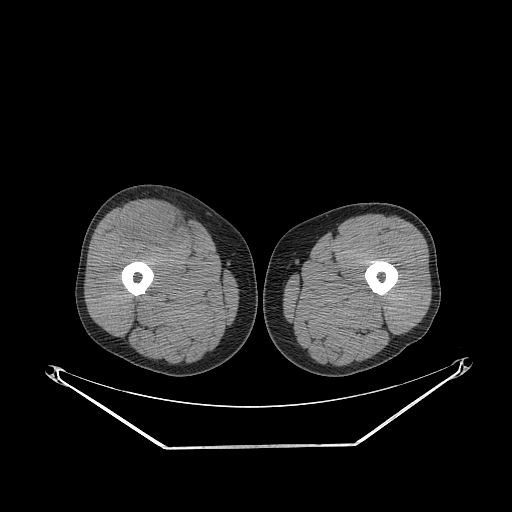
CT of an extremity soft-tissue mass (from a PET/CT study), one axial slice; slice 268 of 311 in the series (ordered by position); reconstruction kernel STANDARD; soft-tissue window (W 400 / L 40 HU); 3.75 mm slice thickness; 512 × 512 image matrix, field of view 500 × 500 mm. Male patient. From the clinical record (not read from this slice): histological type: pleiomorphic leiomyosarcoma; grade: intermediate; site of the primary tumour: right thigh.
Outlined on this slice (expert contour drawn on MRI and transferred to this co-registered scan by the dataset authors):
- gross tumour volume including surrounding oedema: bounding box [x1, y1, x2, y2] px = [125, 205, 181, 250]
- gross tumour volume (mass): [130, 208, 179, 248]